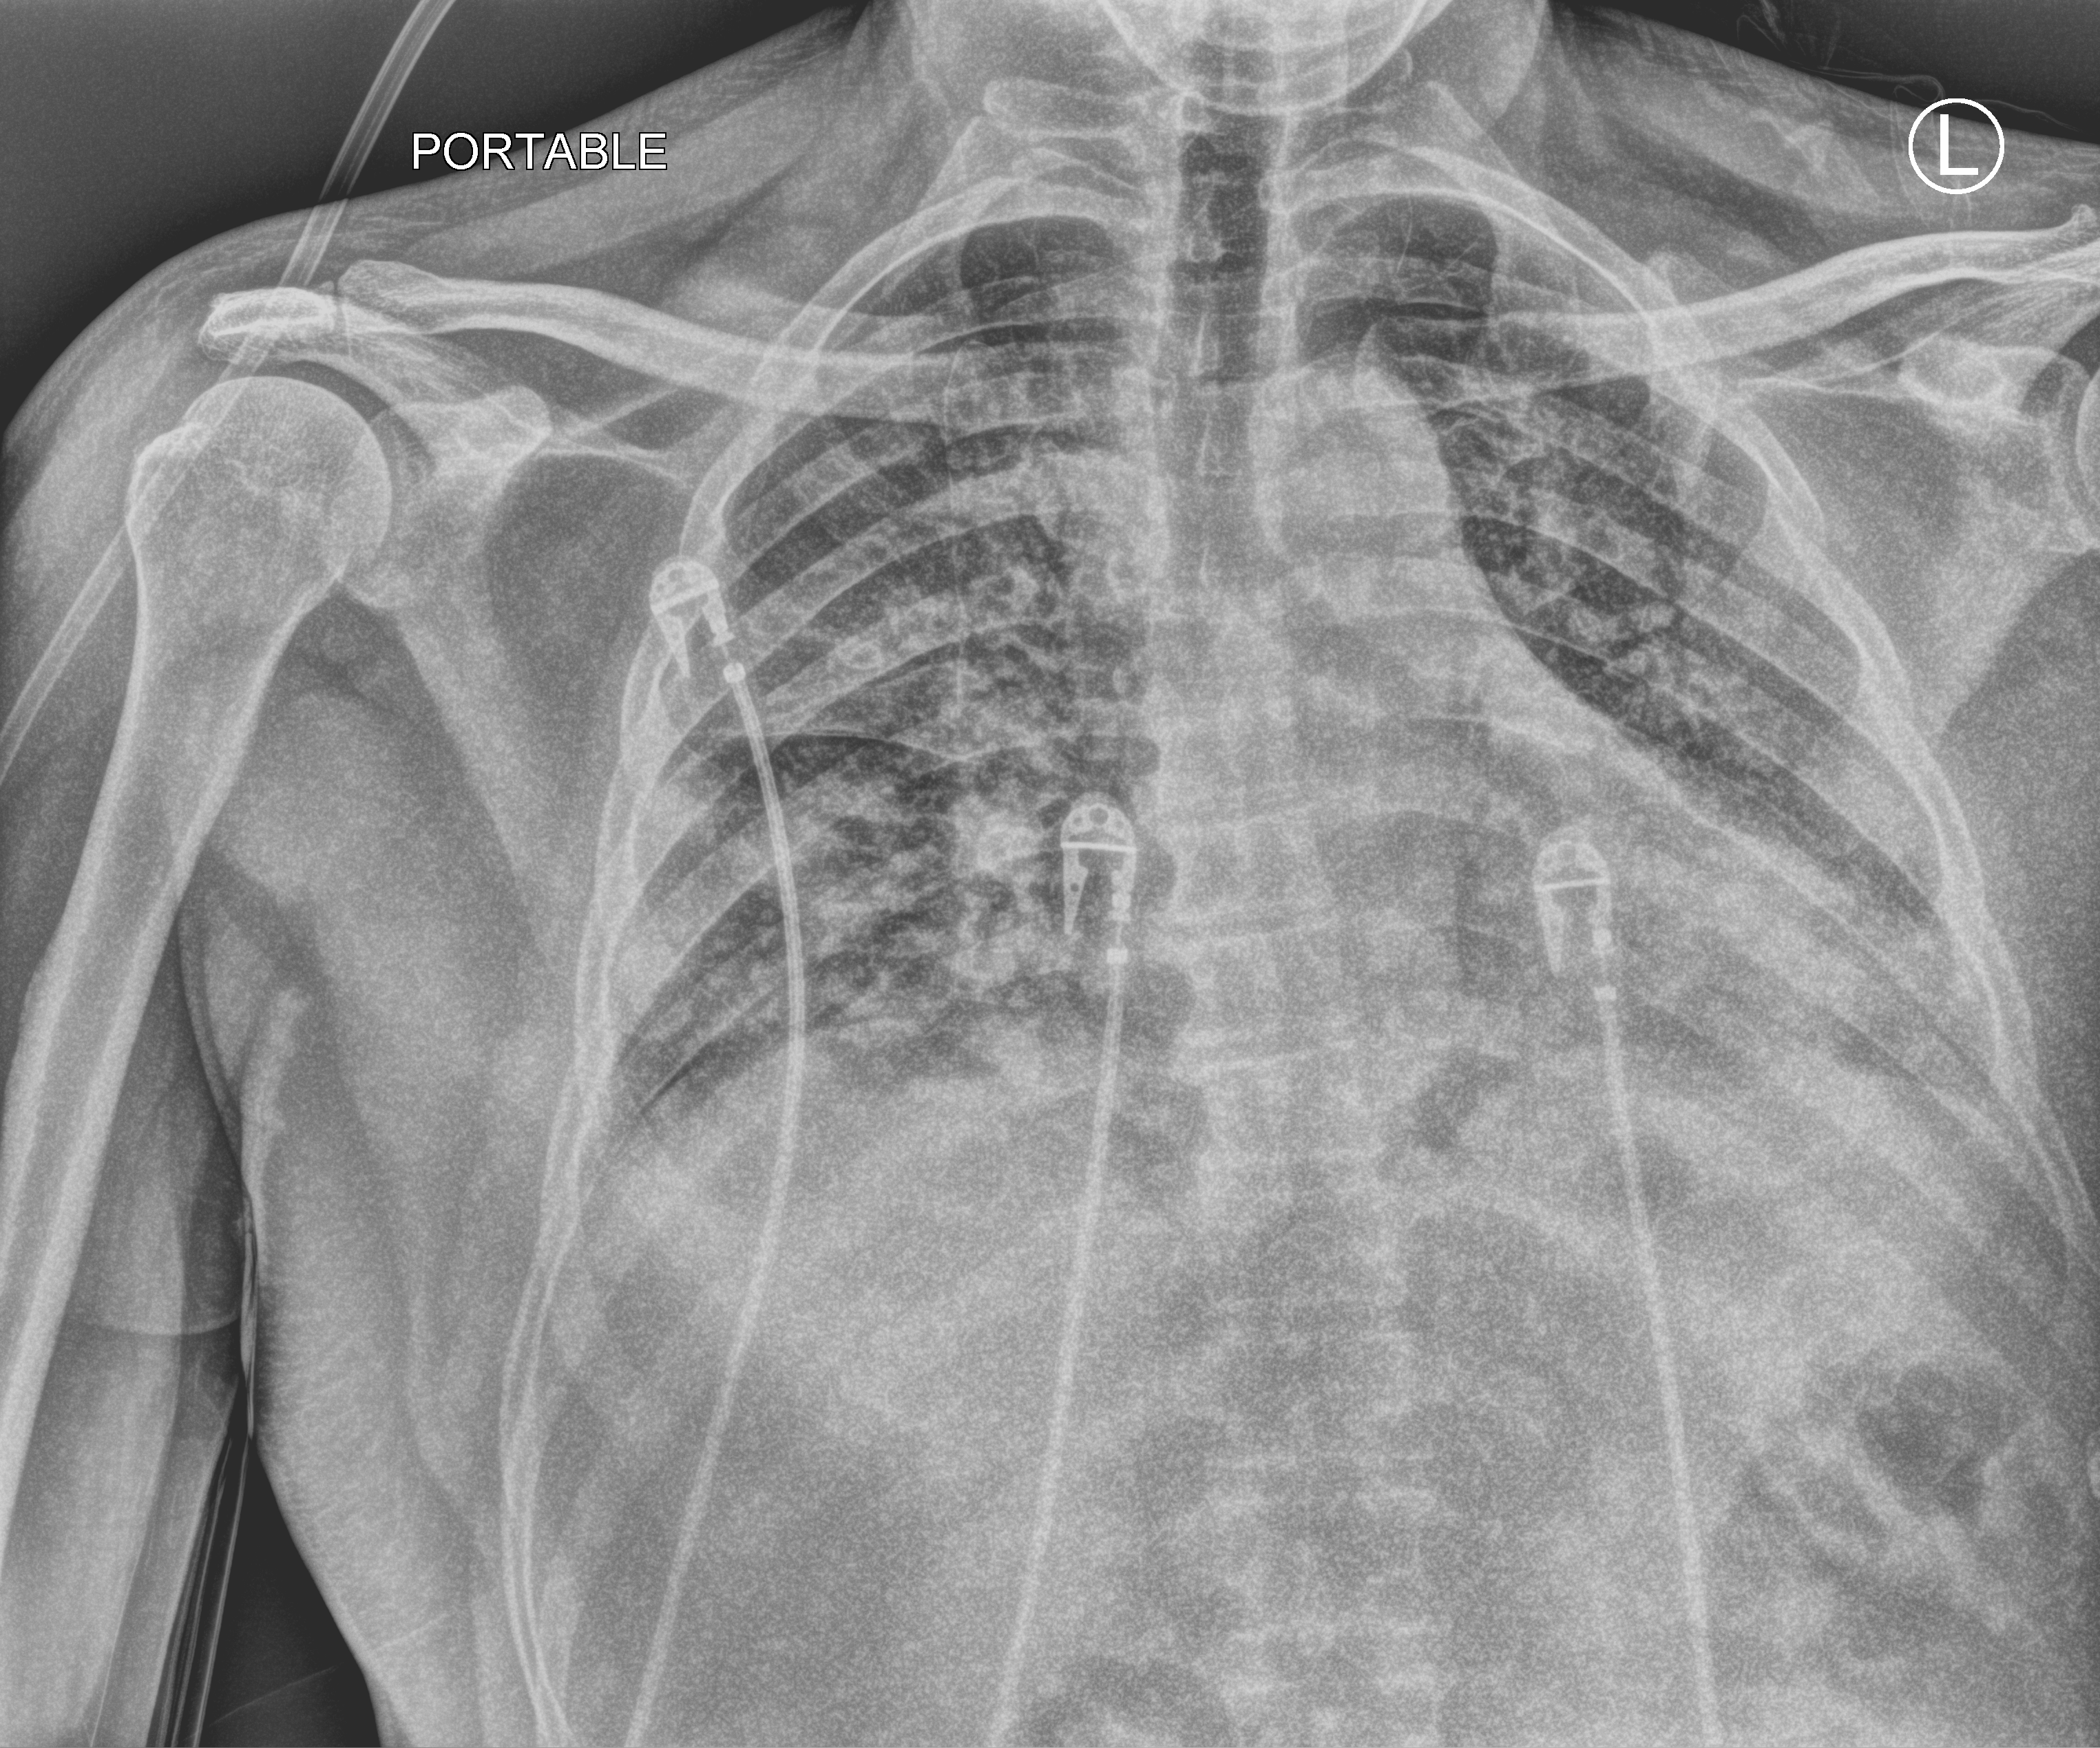
Portable chest radiograph, anteroposterior (AP) projection. Patient hospitalised with COVID-19; male, aged 18–59 years.
Admission-level facts for this patient (not findings on this image; timing relative to this image not recorded):
- mechanically ventilated during this hospital stay: yes
- admitted to intensive care during this hospital stay: yes
- chronic kidney disease (admission record): no